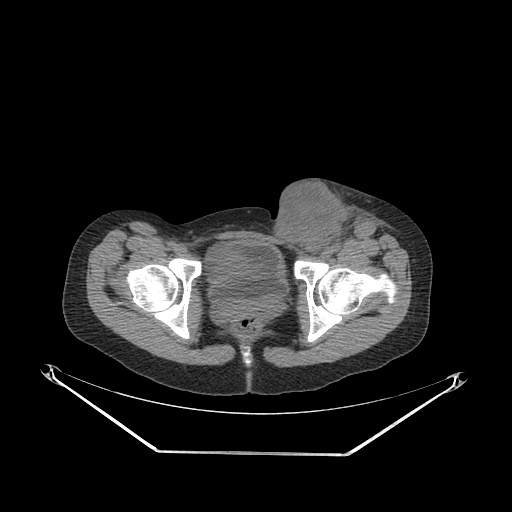
CT of an extremity soft-tissue mass (from a PET/CT study), one axial slice; slice 69 of 267 in the series (ordered by position); reconstruction kernel SOFT; 140 kVp; soft-tissue window (W 400 / L 40 HU); 512 × 512 image matrix. Female patient. Case-level facts recorded for this patient, not image findings: histological type: leiomyosarcoma; grade: high; site of the primary tumour: groin.
Structures marked on this image (expert contour drawn on MRI and transferred to this co-registered scan by the dataset authors):
- gross tumour volume including surrounding oedema: bounding box <267,184,382,259> (left, top, right, bottom; pixels)
- gross tumour volume (mass): <267,187,348,255>